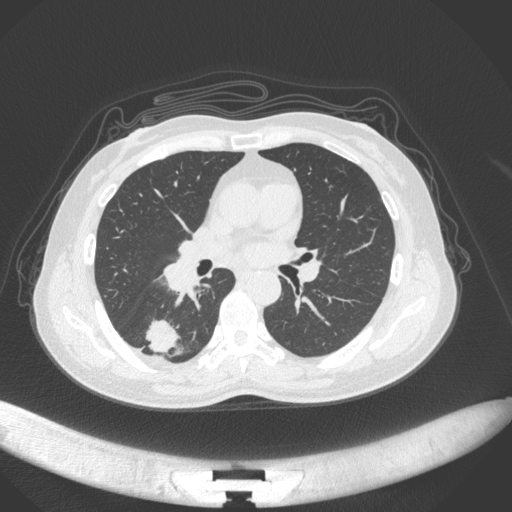
Chest CT, one axial slice. Position 165 of 352 along the scan axis. 120 kVp. Lung window (W 1500 / L -600 HU). 512 × 512 image matrix, field of view 400 × 400 mm. Patient: female, 55 years. Case-level facts recorded for this patient, not image findings: clinical TNM (as recorded): T1c N1 M0.
Structures marked on this image (bounding box drawn by a radiologist):
- lung tumour (recorded histology: adenocarcinoma): bounding box (x1, y1, x2, y2) in pixels: (141, 314, 182, 356)